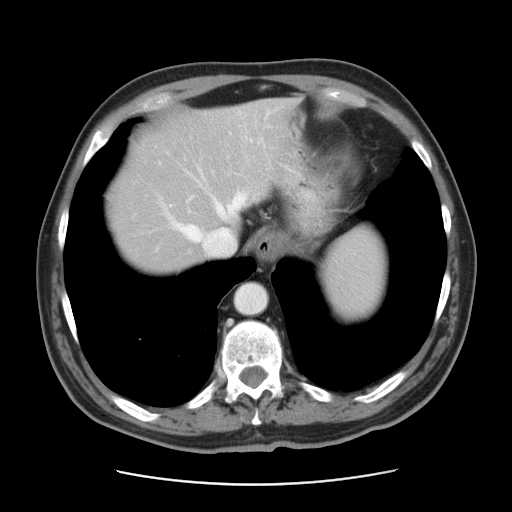
Contrast-enhanced abdominal CT, one axial slice. Slice 36 of 42 in the series (ordered by position). Reconstruction kernel STANDARD. Intravenous contrast given. Soft-tissue window (W 400 / L 40 HU). 5 mm slice thickness. 512 × 512 image matrix. Male patient, age 73 years. From the clinical record (not read from this slice): diagnosis: colorectal cancer liver metastases, imaged before liver resection.
Structures marked on this image (manually delineated by an expert):
- hepatic veins: bounding box <156,165,247,255> (left, top, right, bottom; pixels)
- liver: <111,100,291,271>
- planned liver remnant (the part of the liver to remain after resection): <139,100,292,229>